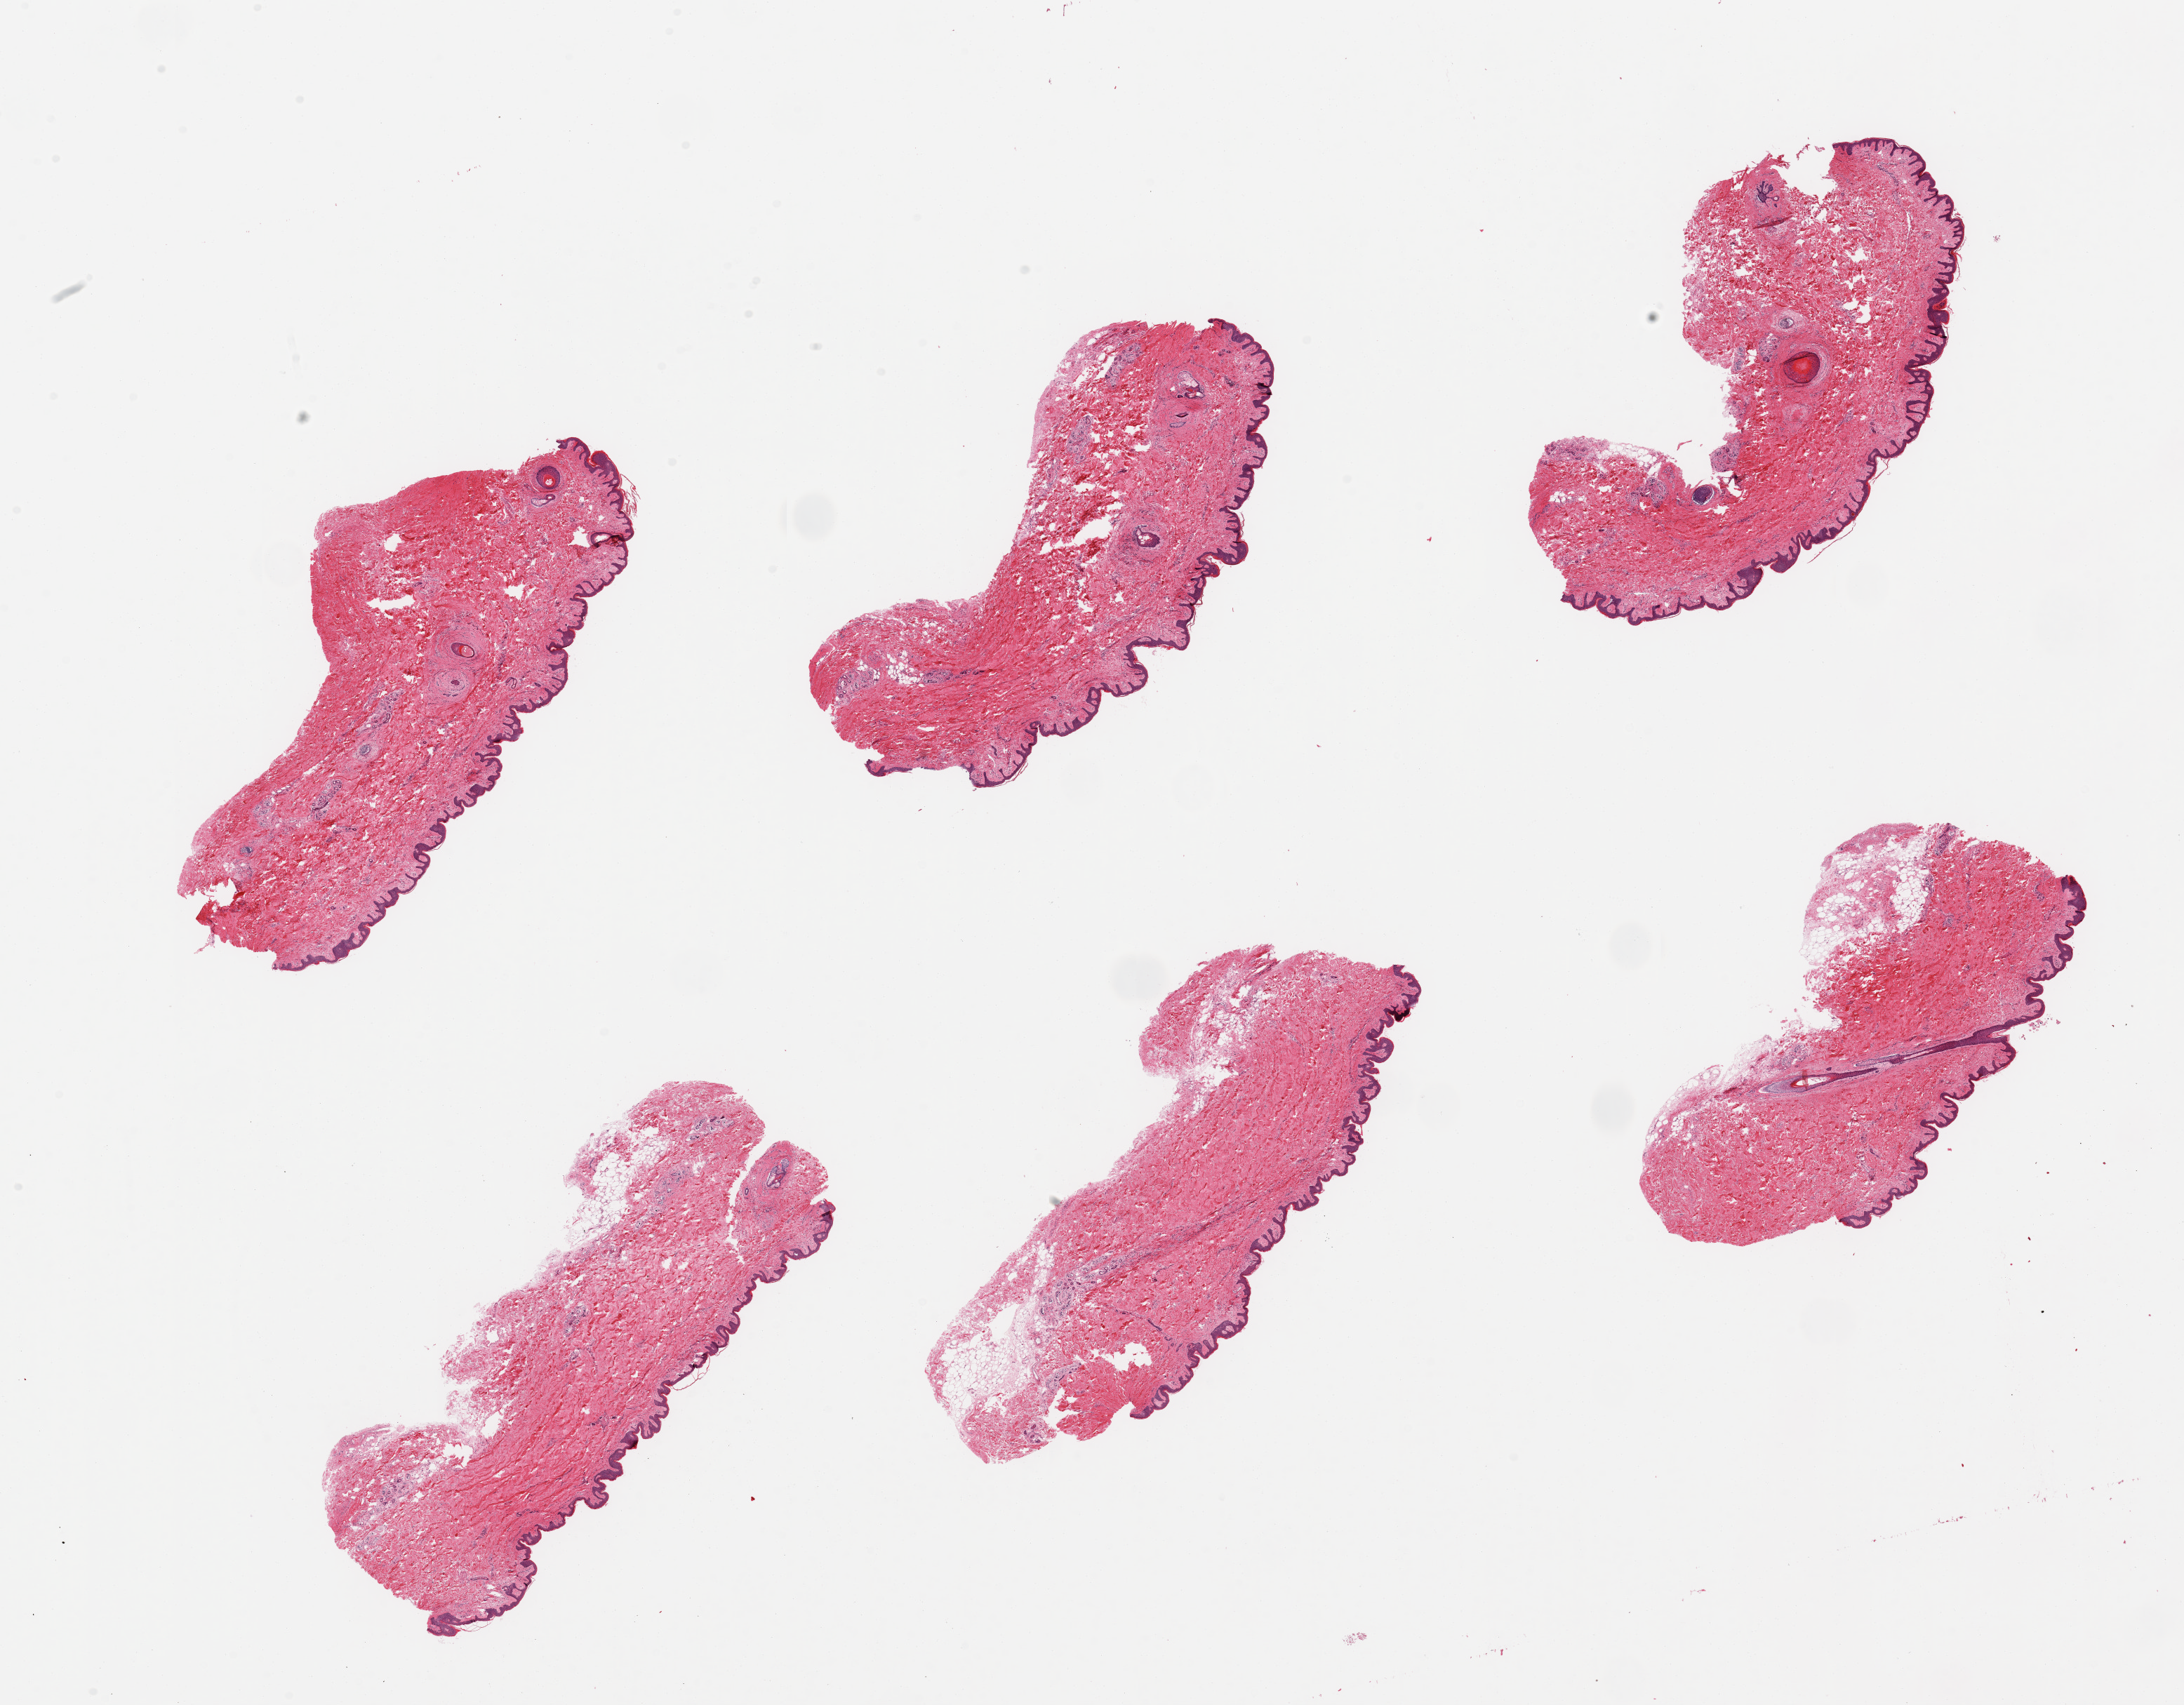
Whole-slide image, haematoxylin and eosin stain, brightfield, a low-resolution overview of the entire scanned area, about 24.6 x 19.2 mm, PAXgene-fixed paraffin-embedded (PFPE) section, section of skin of suprapubic region (target tissue), tissue donor sample. Donor: male.
Review note (as recorded): 6 pieces; some adnexal glands are moderately autolyzed; well trimmed; 10% dermal fat.